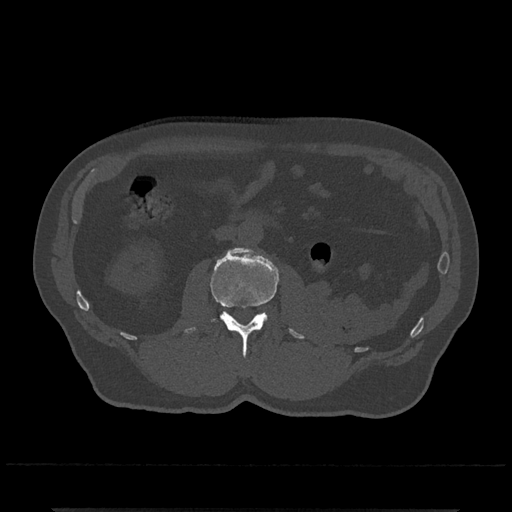
CT including the spine, one axial slice; slice 285 of 797 in the series (ordered by position); reconstruction kernel Br40s/3; bone window (W 1800 / L 400 HU); 0.5 mm slice thickness; 512 × 512 image matrix. Male patient, age 67 years. From the clinical record (not read from this slice): primary cancer: prostate.
Outlined on this slice (semi-automatically segmented with operator editing):
- L2 vertebra: bounding box [x1, y1, x2, y2] px = [184, 247, 305, 358]
- L3 vertebra: [259, 312, 264, 315]